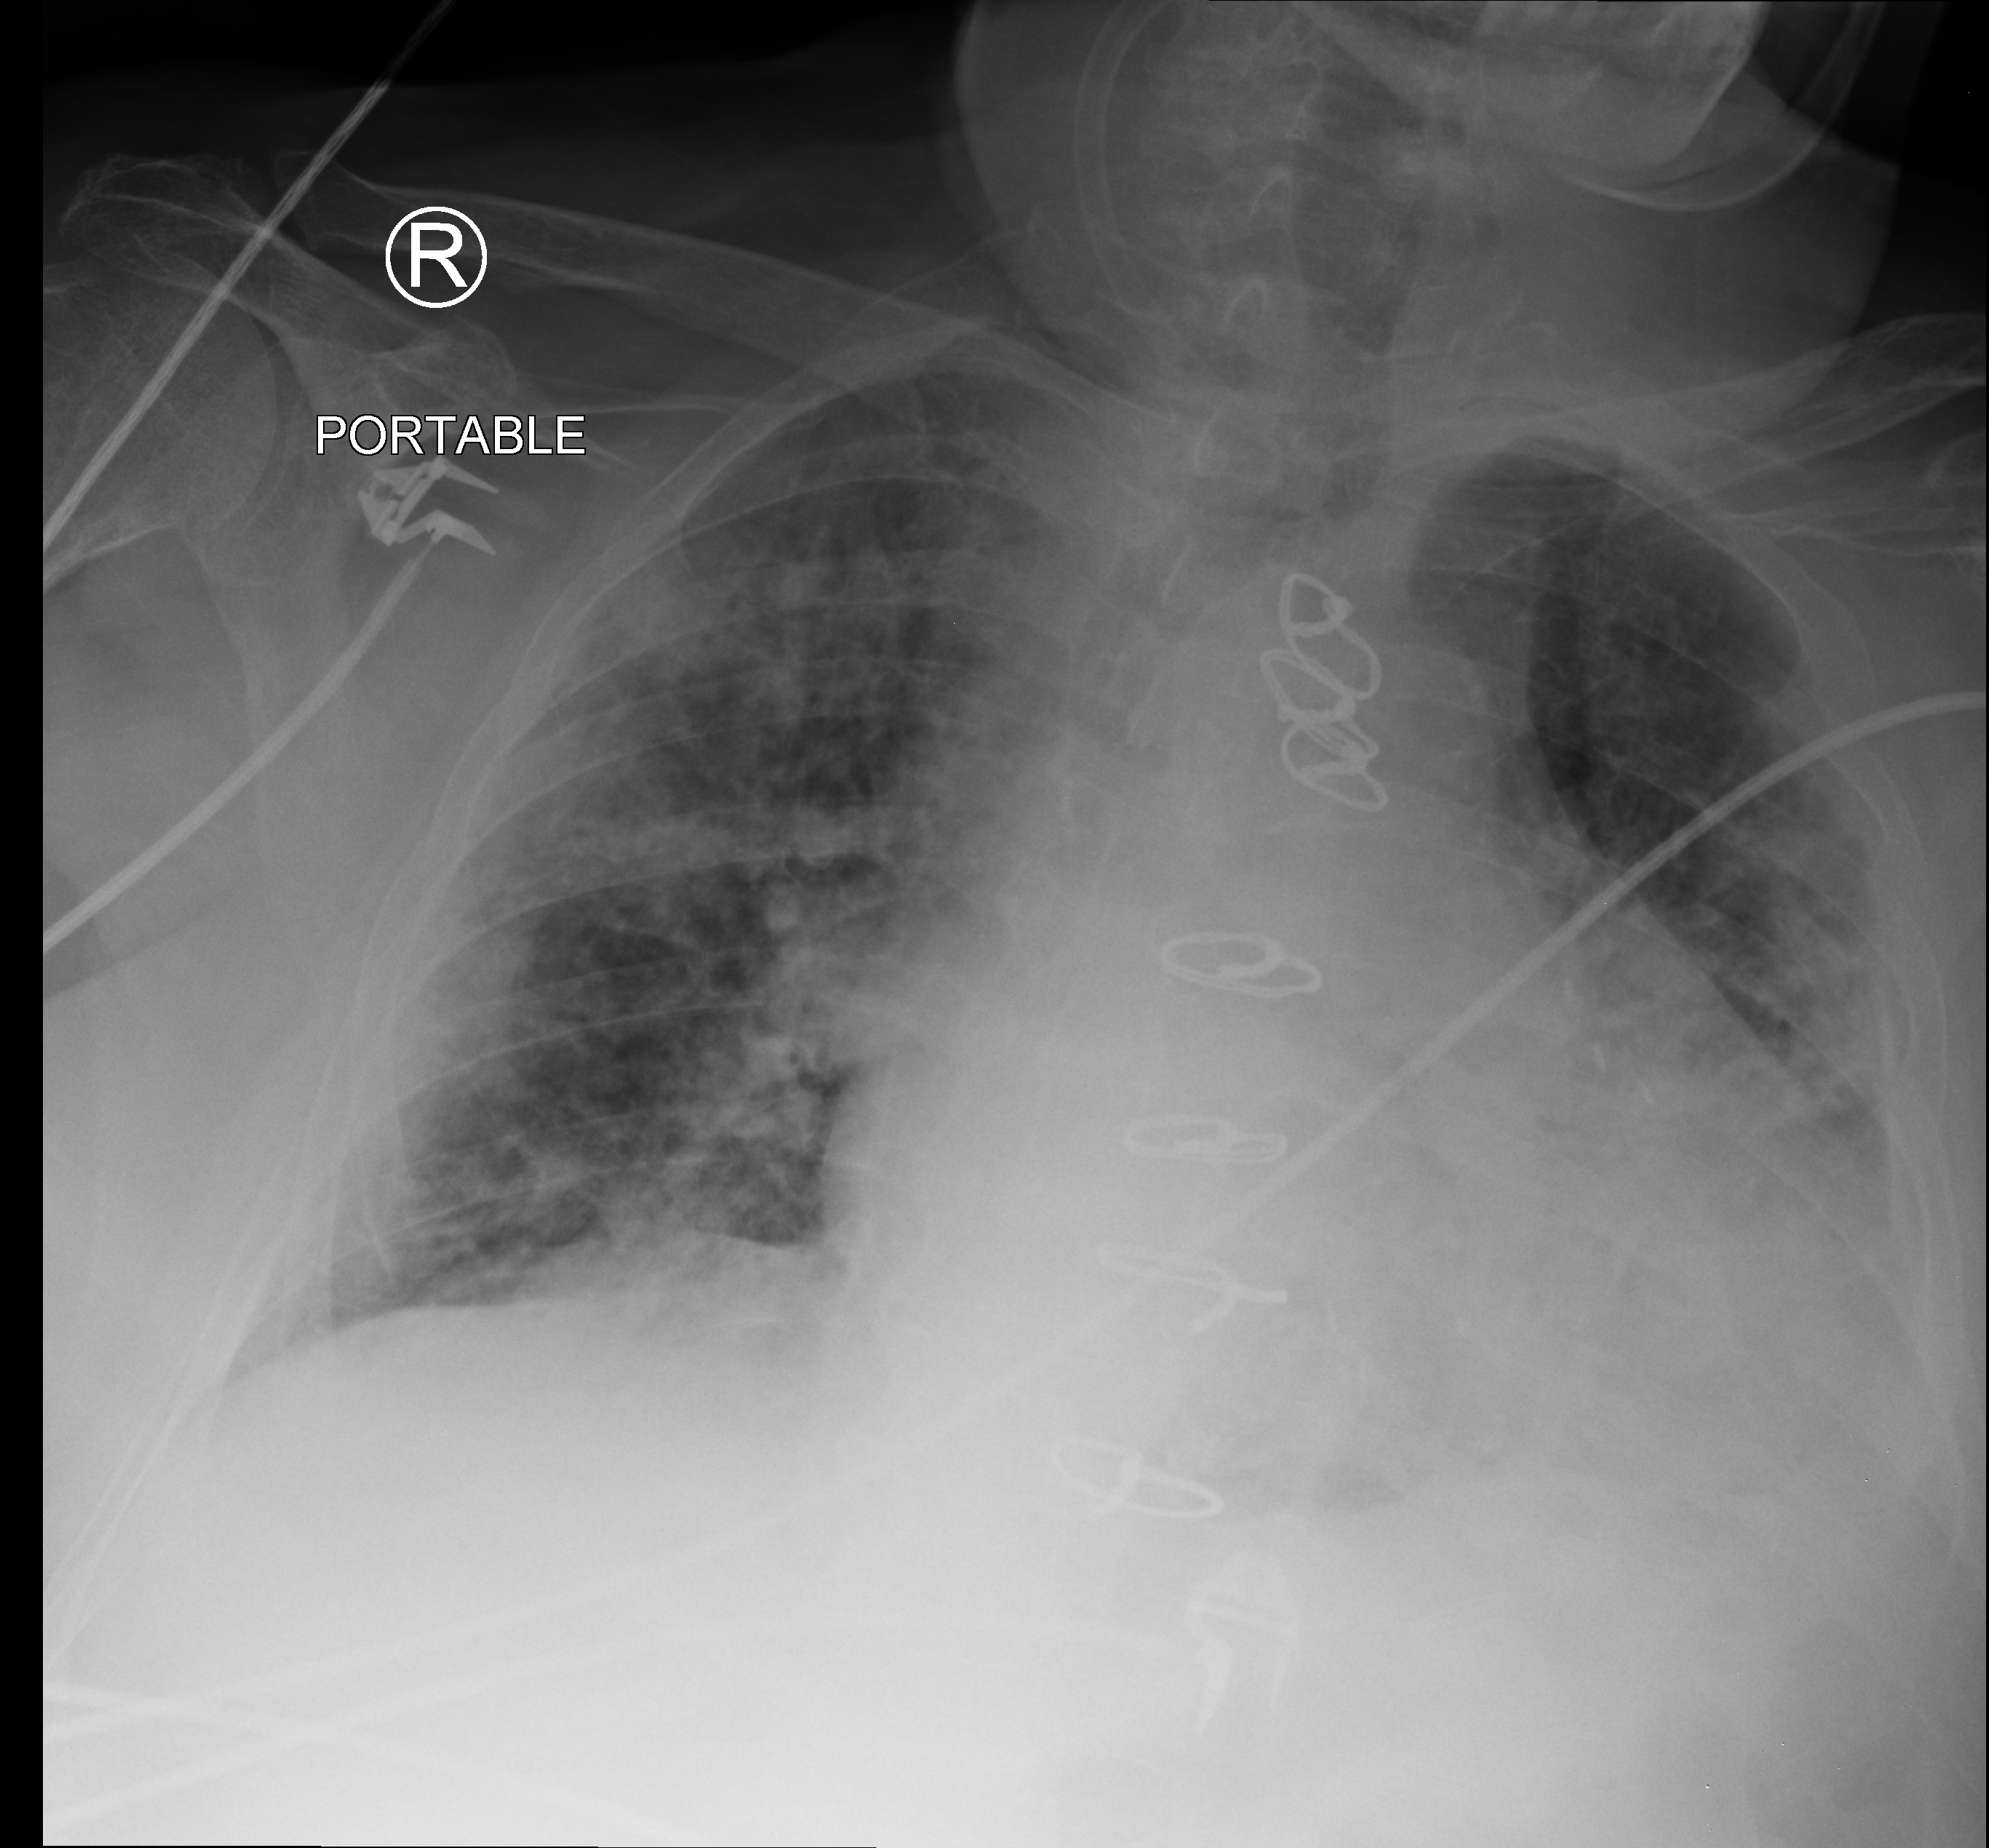
Chest X-ray (portable); anteroposterior (AP) projection. Male patient hospitalised with COVID-19, age 75–90 years.
Hospital-stay facts (about this admission, not read from this image; timing relative to this image not recorded):
- mechanically ventilated during this hospital stay: no